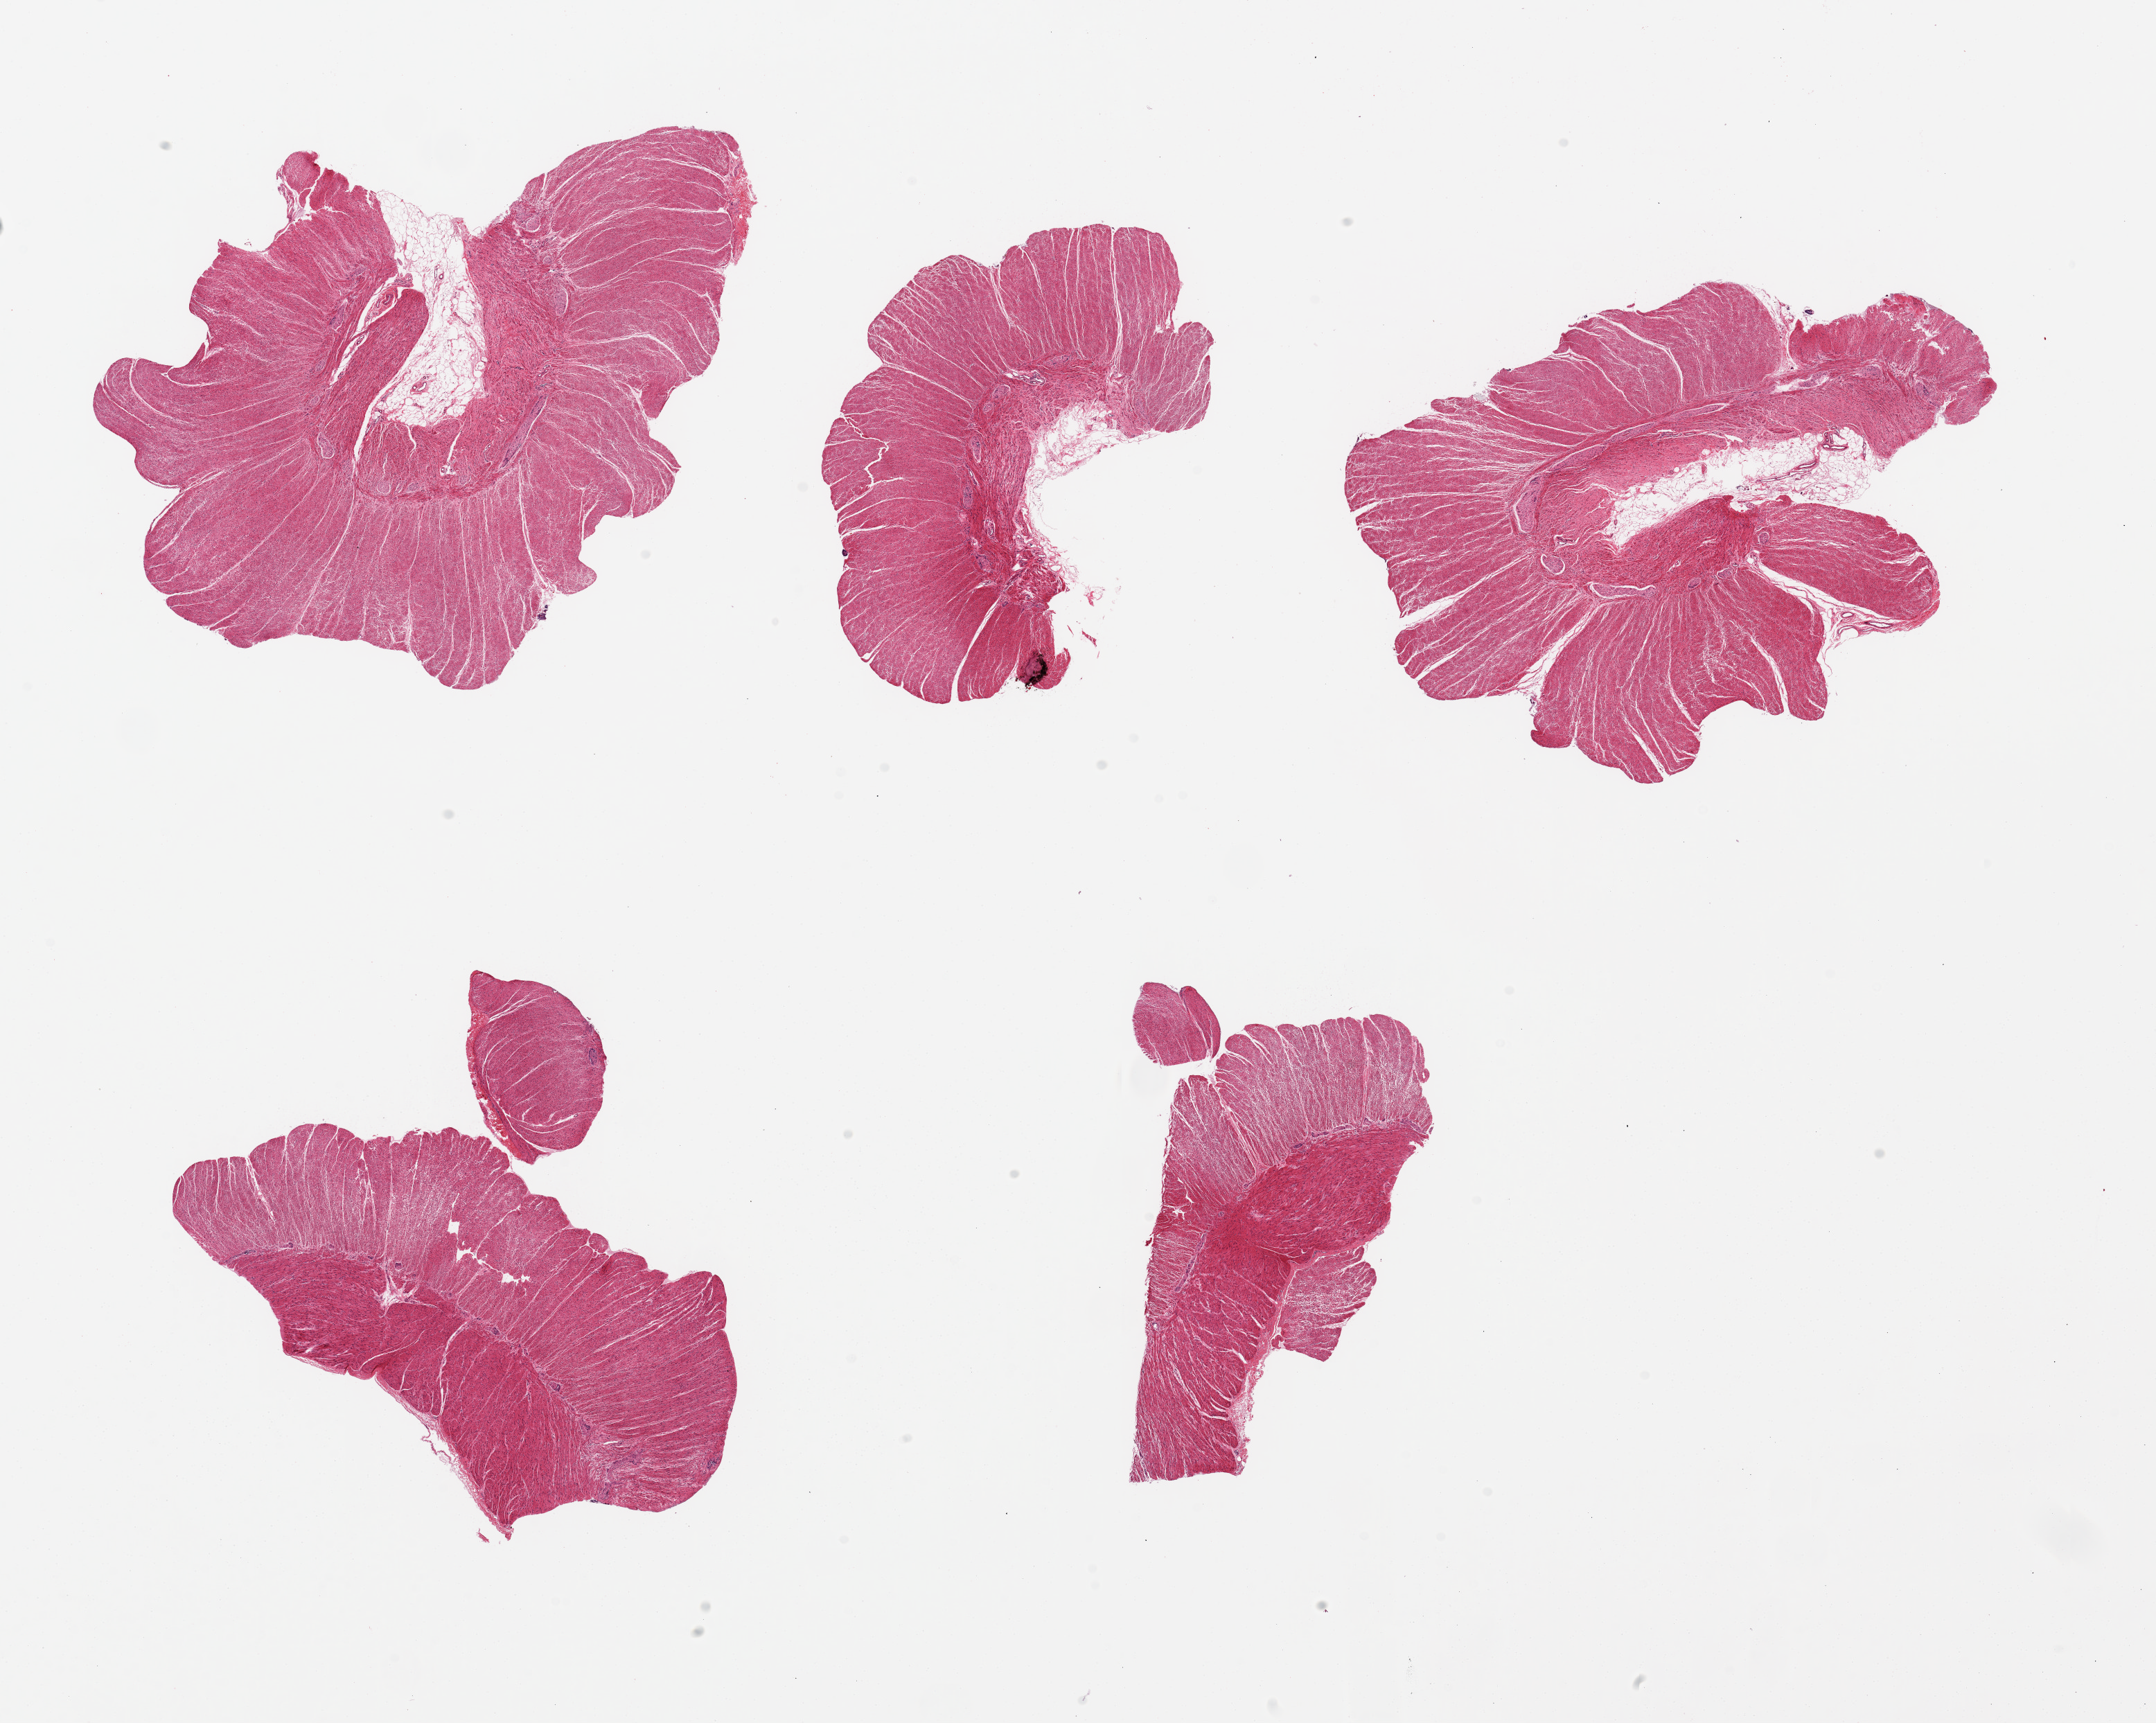
Digitized hematoxylin and eosin (H&E)-stained section — low-resolution overview of the scanned area, about 24.6 x 19.7 mm; PAXgene-fixed paraffin-embedded (PFPE) section; target tissue: sigmoid colon; donor tissue sample. Donor: male.
* pathologist's review note for this sample: 5 pieces ~6x3mm. All muscle, excellent specimens